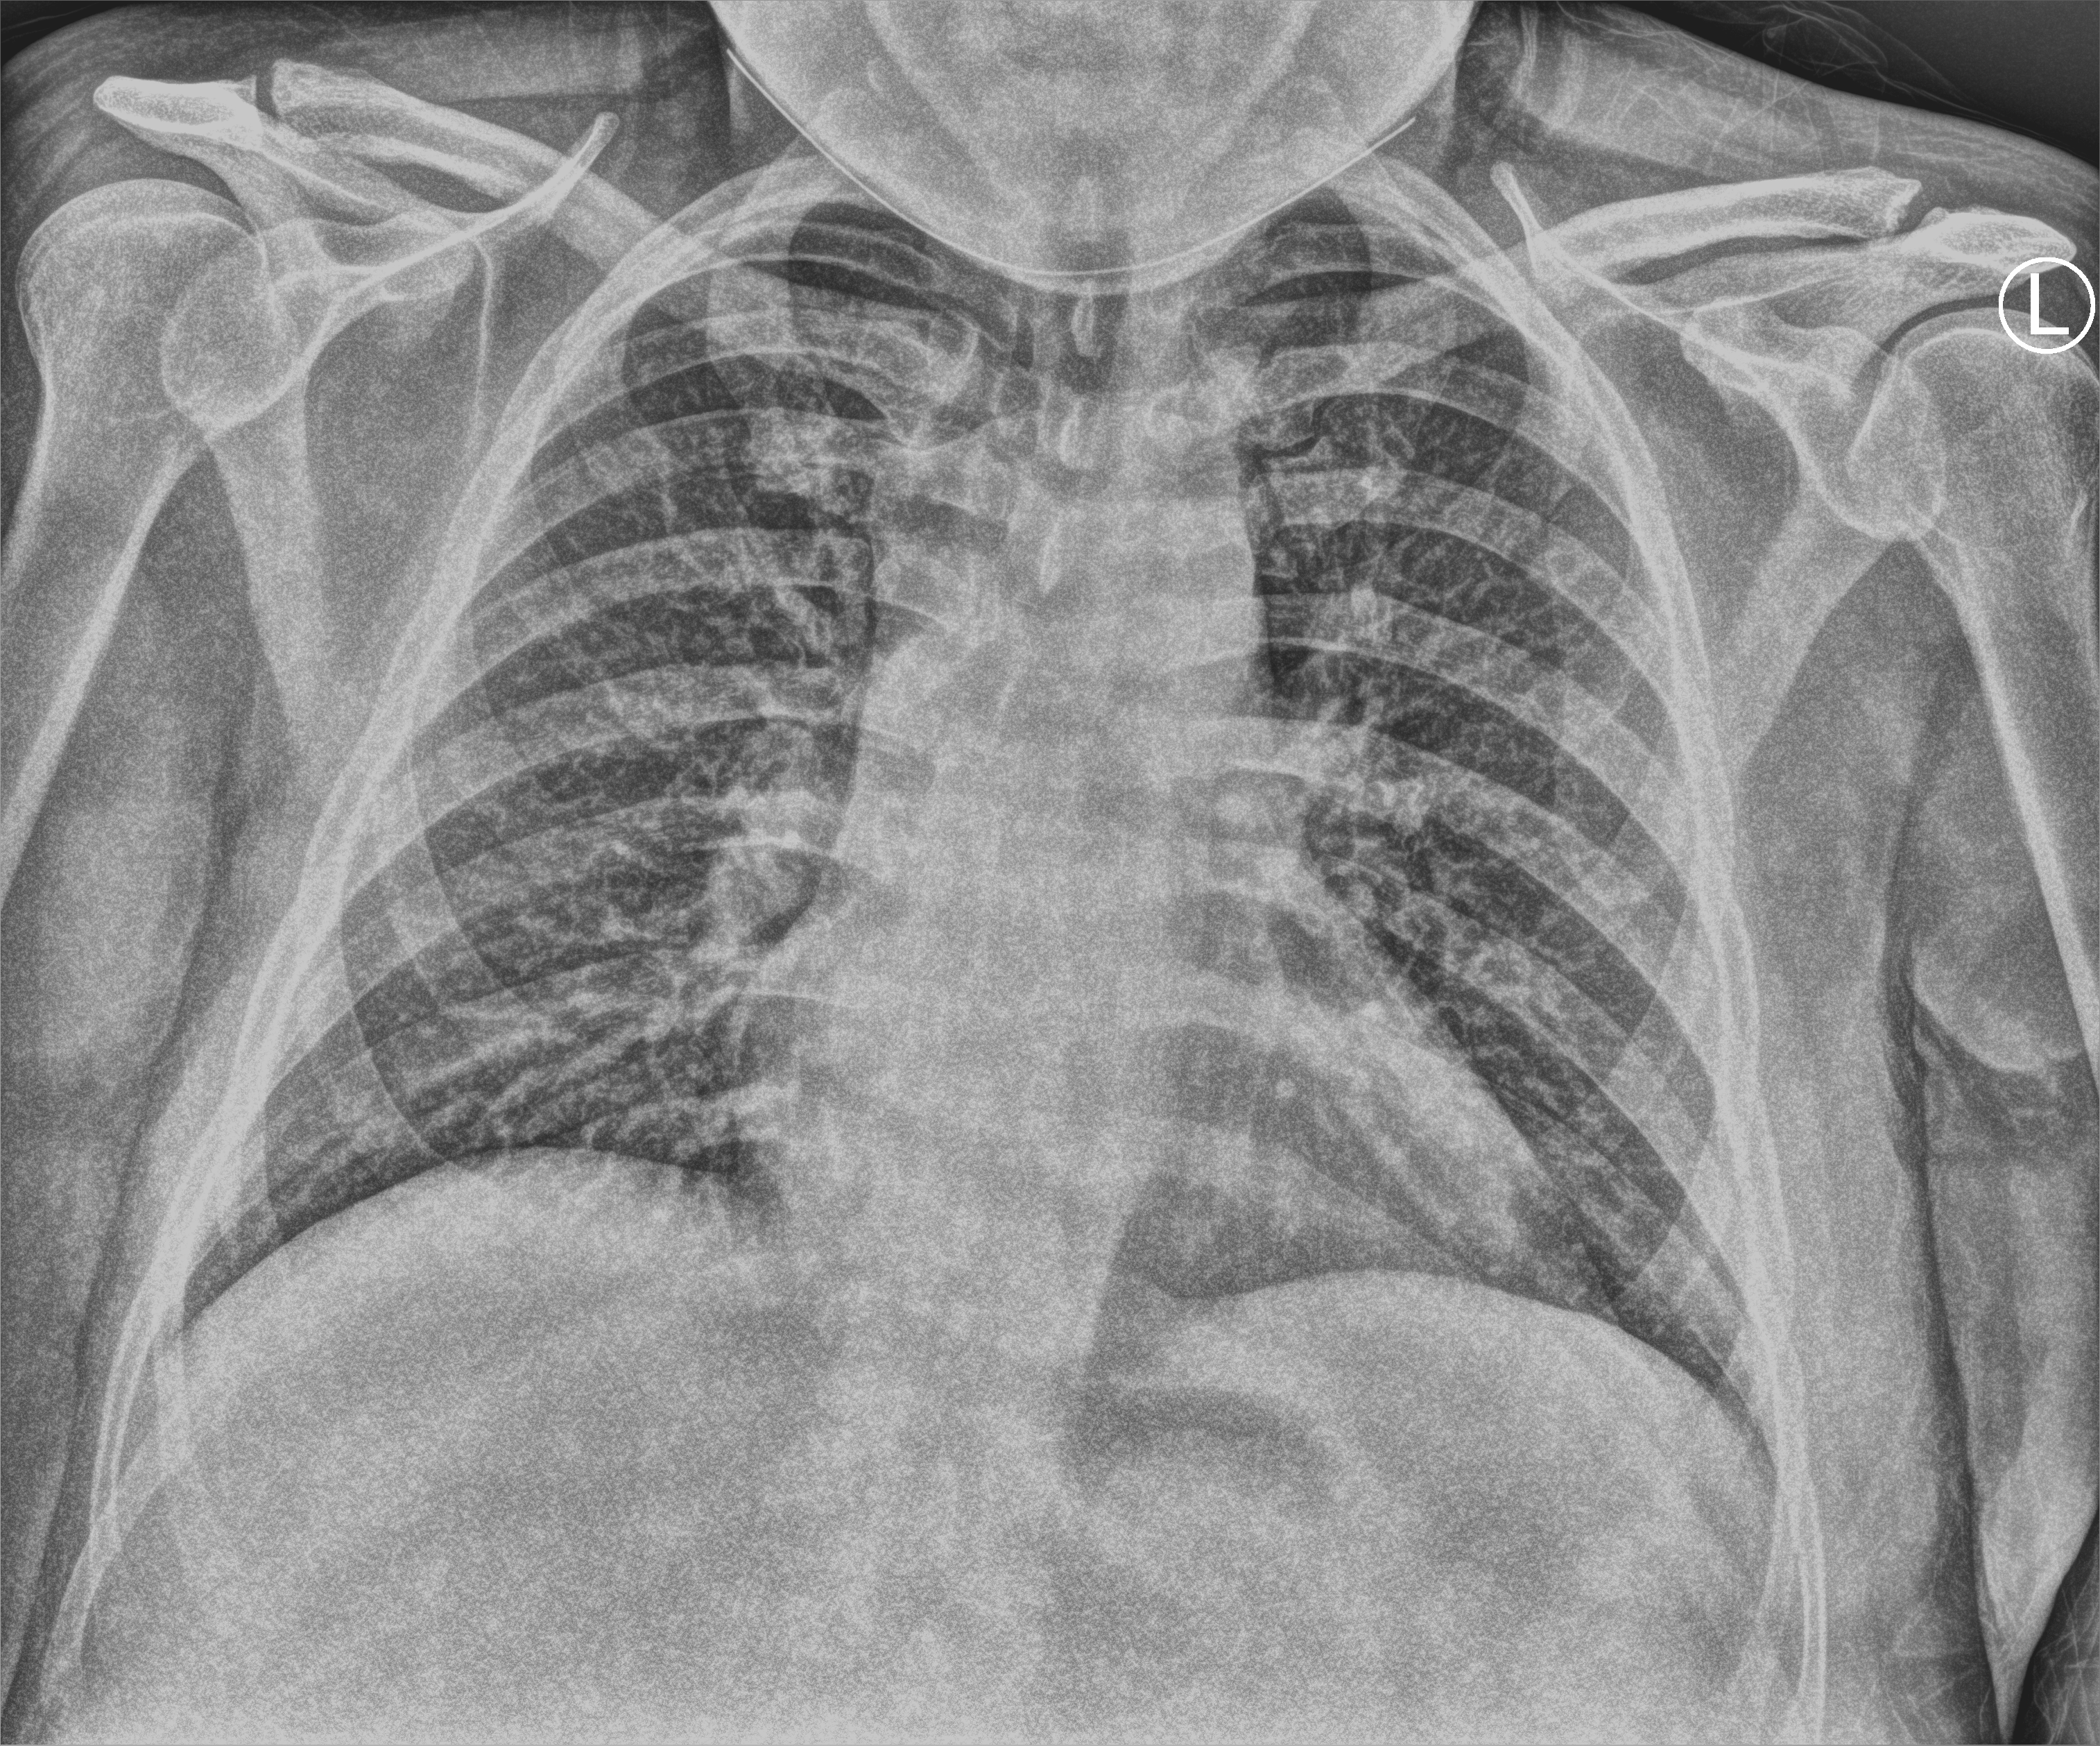
Chest X-ray (portable), anteroposterior (AP) projection. Patient hospitalised with COVID-19; male, aged 18–59 years.
From the hospital-stay record, not from the radiograph (when in the stay this image was taken is not recorded): admitted to intensive care during this hospital stay: no.